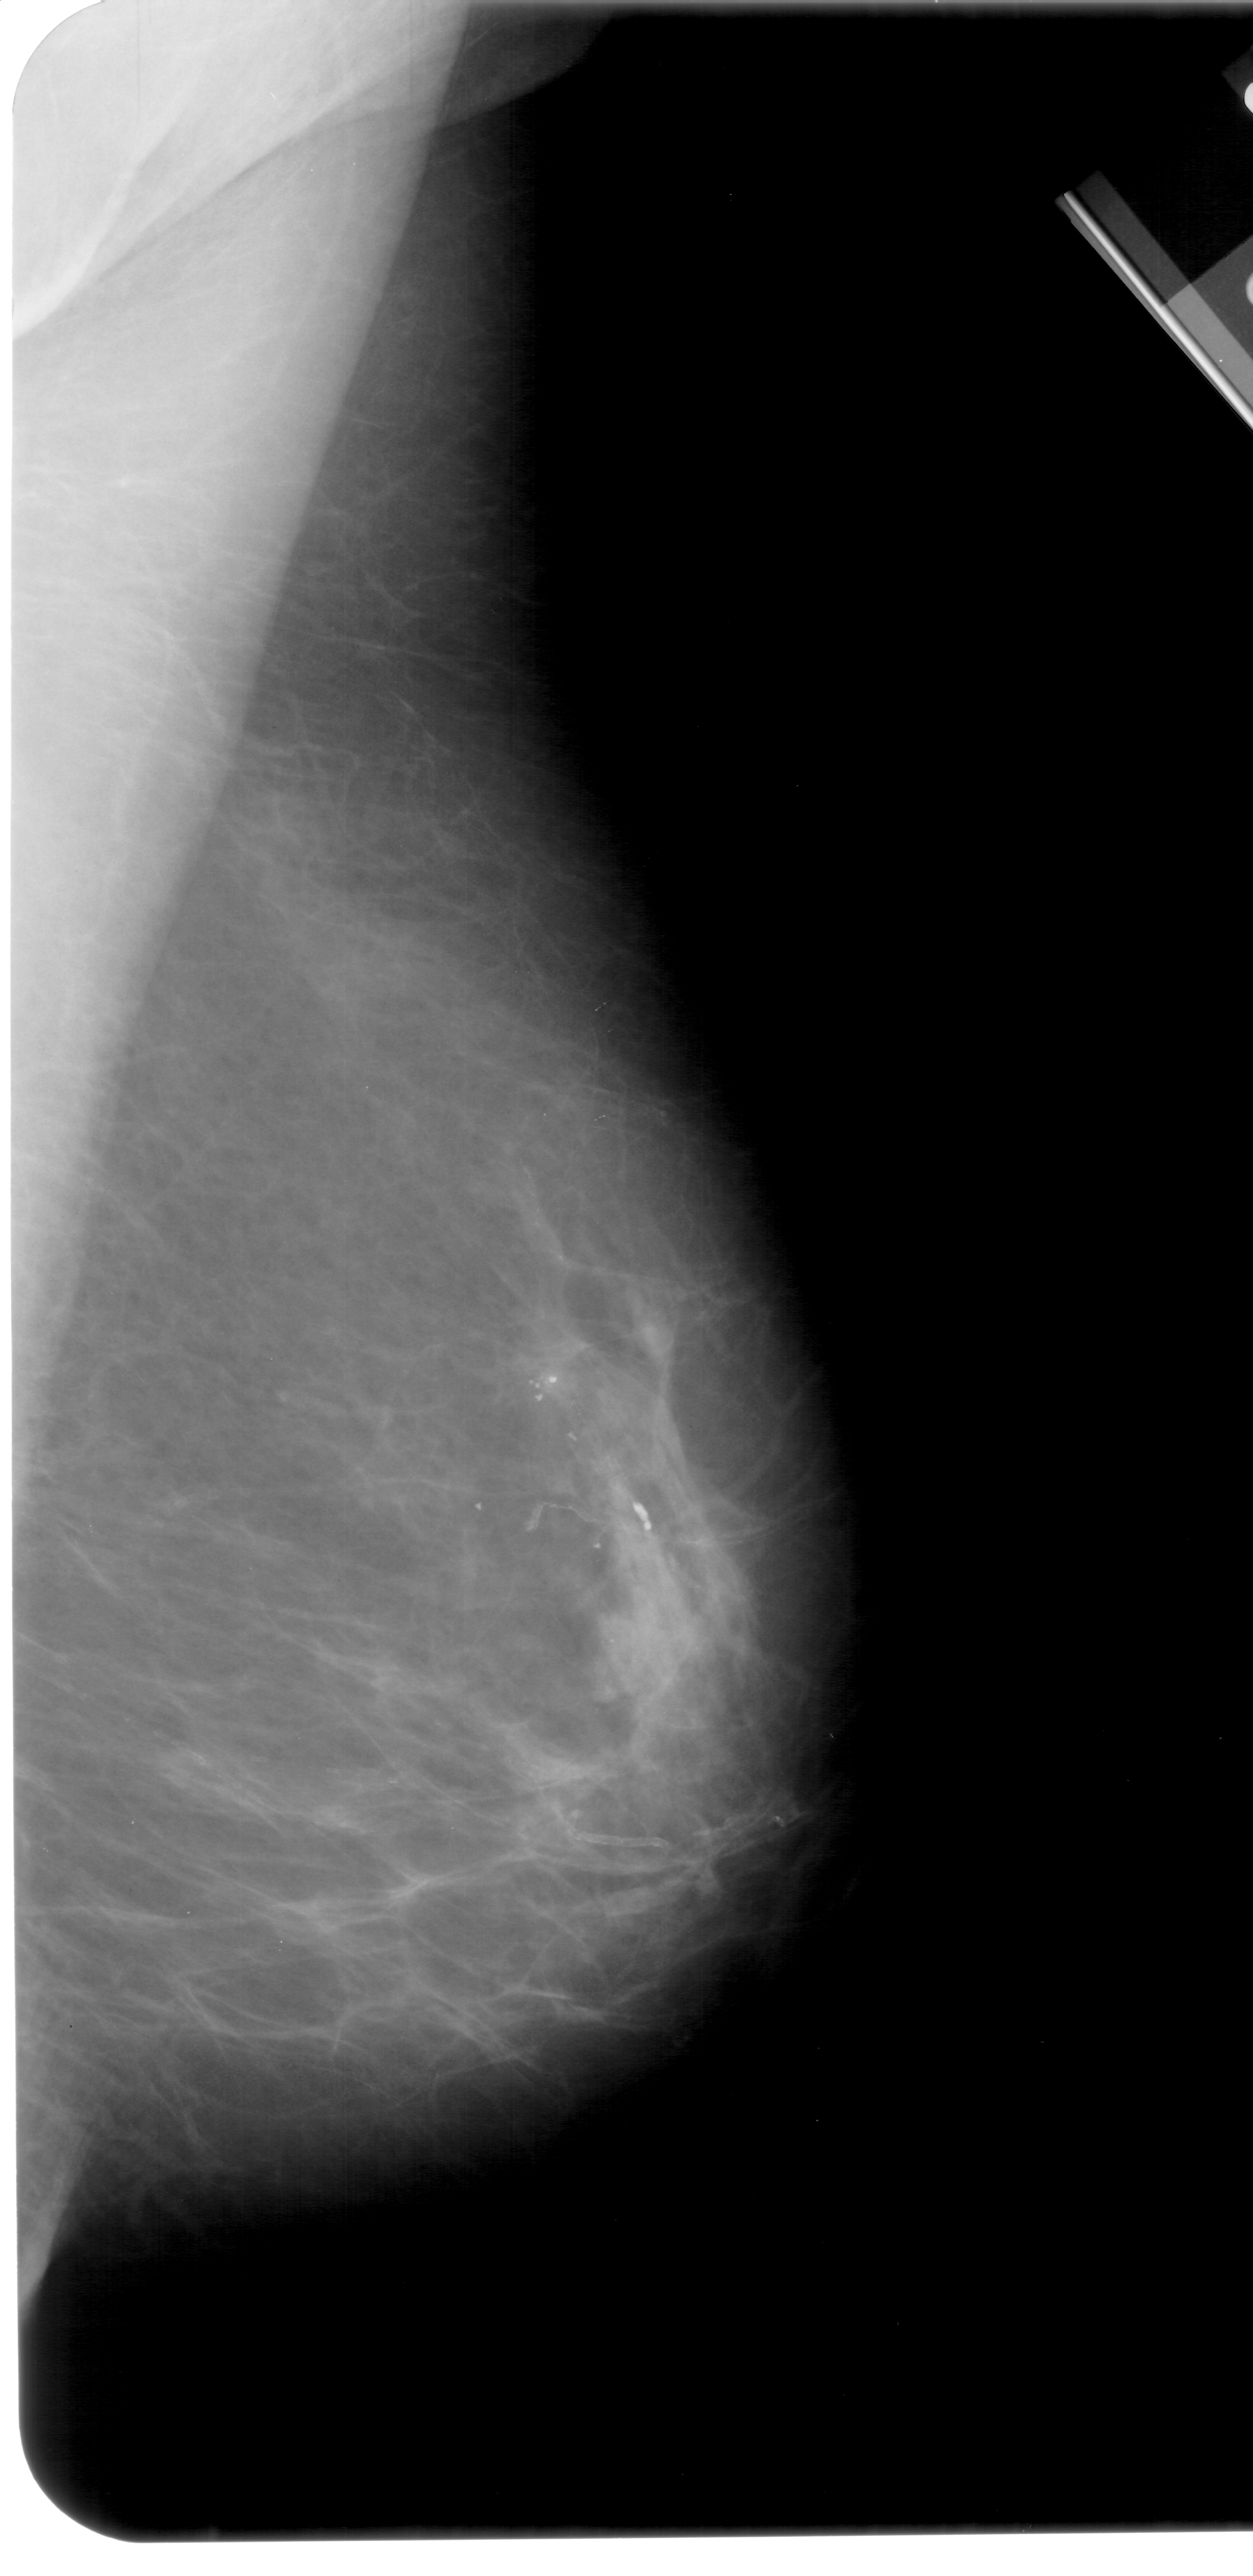
Digitized screen-film mammogram, right breast, MLO view.
Abnormality record for this image: calcifications, morphology pleomorphic, distribution linear; BI-RADS assessment category 4; pathology (as recorded): malignant.